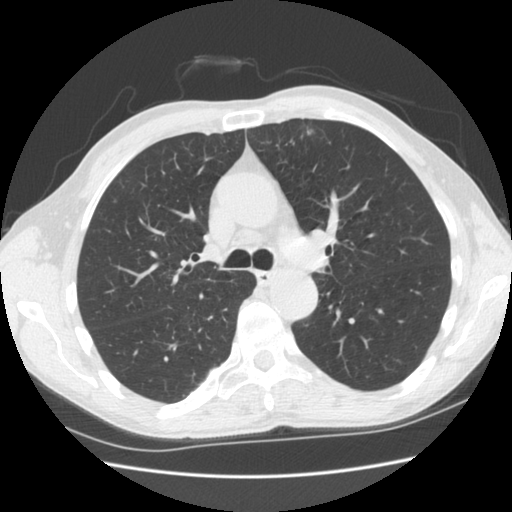
Low-dose screening chest CT, one axial slice; position 112 of 169 along the scan axis; 120 kVp; lung window (W 1500 / L -600 HU); 2.5 mm slice thickness; 512 × 512 image matrix, field of view 340 × 340 mm.
Outlined on this slice (expert manual segmentation):
- lesion 1 (tumor, upper lobe of left lung): bounding box <306,125,314,135> (left, top, right, bottom; pixels)